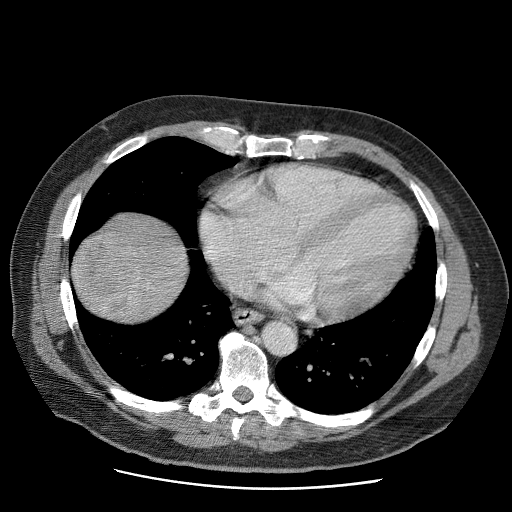
Contrast-enhanced abdominal CT (liver protocol), one axial slice; slice 64 of 81 in the series (ordered by position); reconstruction kernel STANDARD; soft-tissue window (W 400 / L 40 HU); 2.5 mm slice thickness; 512 × 512 image matrix, field of view 380 × 380 mm. From the clinical record (not read from this slice): diagnosis: hepatocellular carcinoma (patient treated with transarterial chemoembolisation; whether this scan precedes or follows treatment is not stated here); TNM stage (as recorded): Stage-IIIA; Child-Pugh class: A; tumour differentiation: moderately differentiated; tumour nodularity: multinodular.
Structures marked on this image (semi-automatic segmentation, software-assisted and operator-edited):
- liver parenchyma outside the tumour (the mass and vessels are separate outlines, so this box may not span the whole liver): box from (x=72, y=212) to (x=186, y=320) px
- mass: (x=71, y=231)–(x=143, y=320)